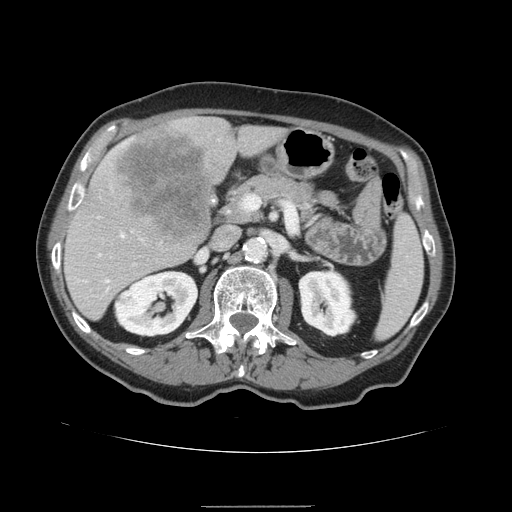
Contrast-enhanced abdominal CT, one axial slice. Position 76 of 168 along the scan axis. 120 kVp. Intravenous contrast given. Soft-tissue window (W 400 / L 40 HU). 2.5 mm slice thickness. 512 × 512 image matrix, field of view 386 × 386 mm. Male patient, age 74 years. From the clinical record (not read from this slice): diagnosis: colorectal cancer liver metastases, imaged before liver resection; multiple liver metastases: no; largest metastasis: 14.5 cm; chemotherapy before resection: no.
Structures marked on this image (outlined manually by an expert reader):
- hepatic veins: bounding box <121,234,124,237> (left, top, right, bottom; pixels)
- liver: <64,117,287,321>
- planned liver remnant (the part of the liver to remain after resection): <64,125,286,321>
- liver metastasis: <114,125,213,243>